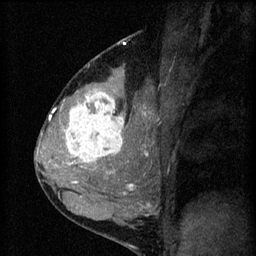
Breast MRI (dynamic contrast-enhanced), one sagittal slice; slice 36 of 60 in the series (ordered by position); 3 images stored at this slice position (order not interpretable as contrast timing); 1.5 T; TE 4.2 ms, TR 8.2 ms; 2 mm slice thickness; 256 × 256 image matrix. Female patient, age 37 years.
Annotated regions visible in this slice (semi-automatically segmented with operator editing):
- analysis volume of interest (the breast-tissue region the enhancement analysis was run in; not a lesion): bounding box <53,78,140,181> (left, top, right, bottom; pixels)
- tumour enhancement mask (voxels above the 70 % enhancement threshold inside the analysis volume of interest): <53,92,124,165>